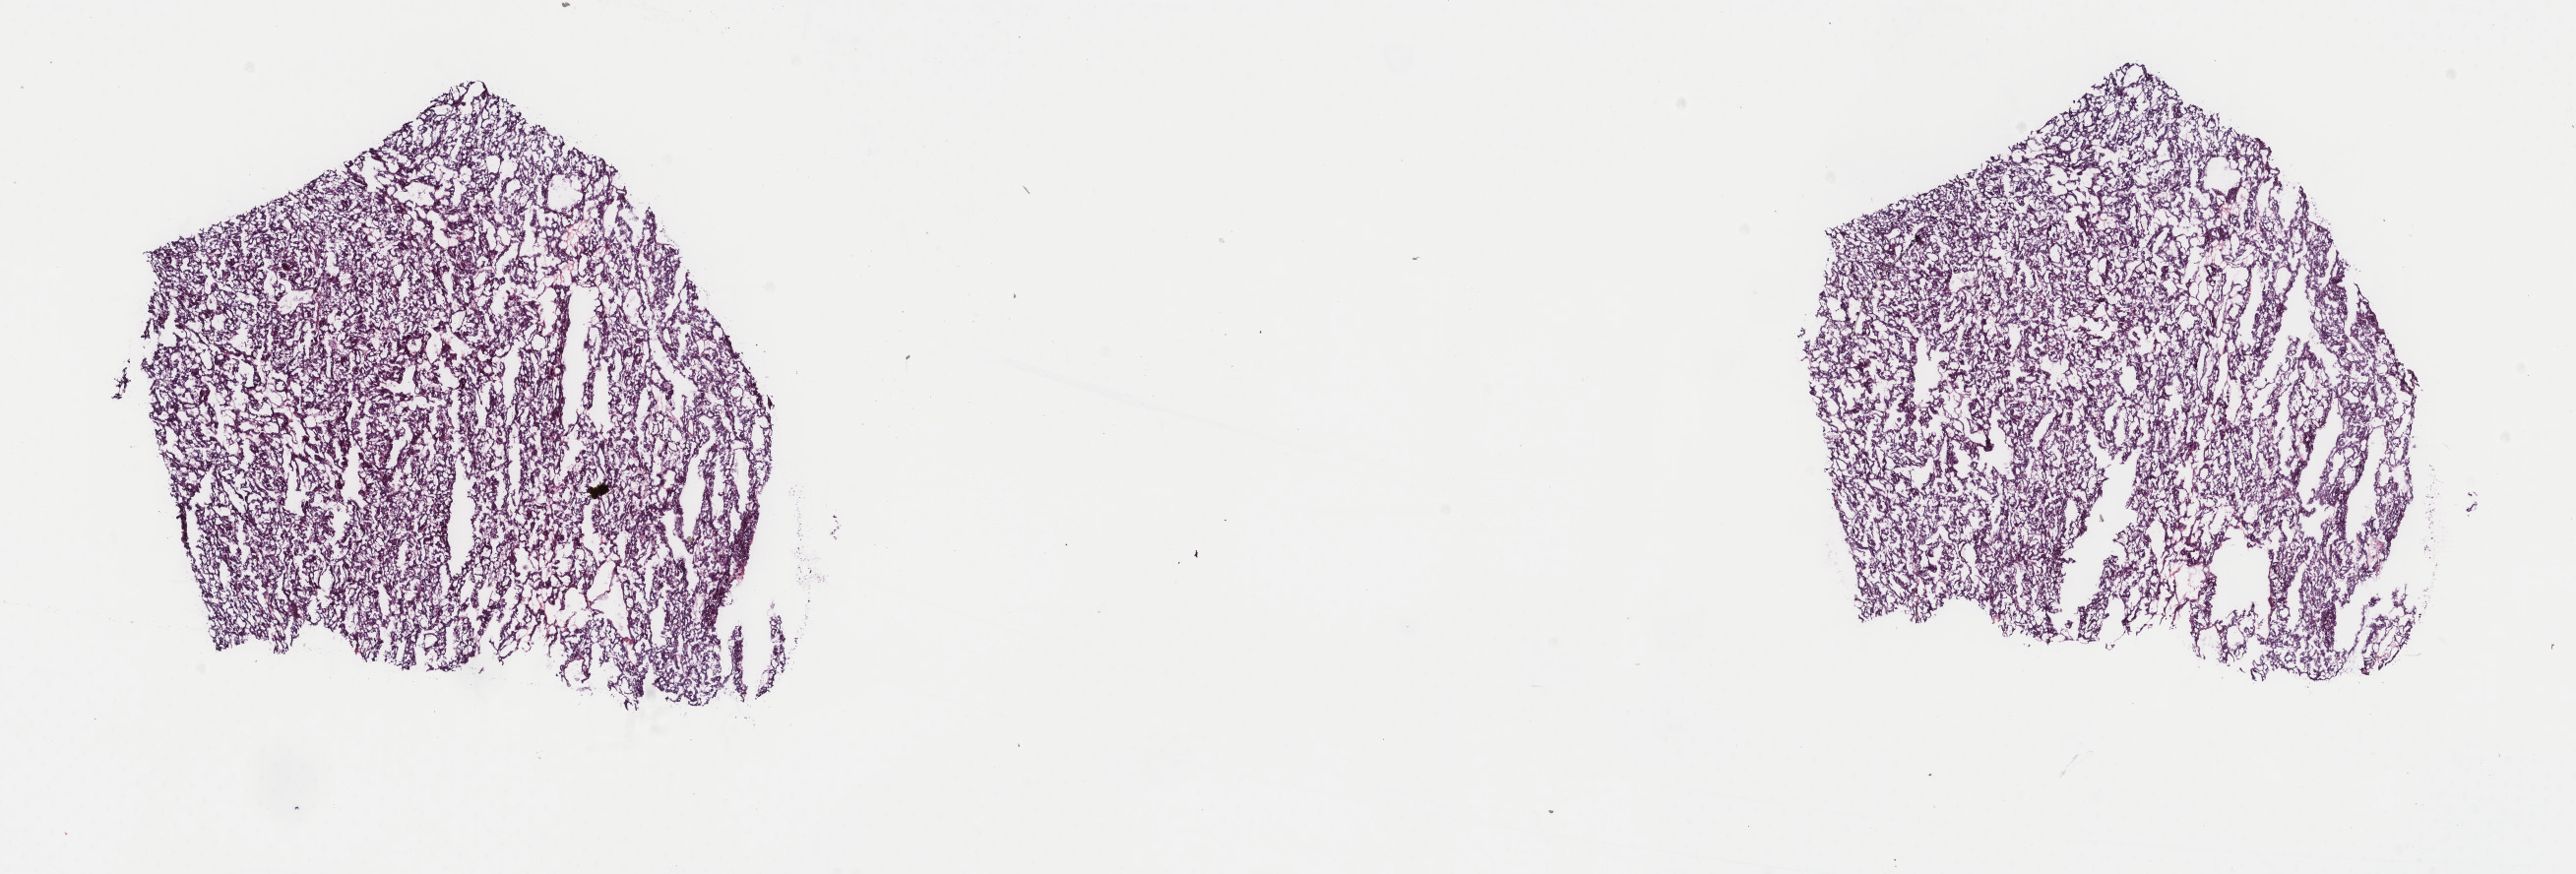
Whole-slide histology image, Hematoxylin and eosin (H&E) stained, shown as a low-resolution overview of the whole scanned area (about 20.8 x 7.0 mm); frozen section from the top of the tissue portion; primary tumour sample from the thyroid. Patient: male, age at initial diagnosis 41 years. Pathologist review of this section (percent, as recorded): tumour cells 90%, tumour nuclei 100%, normal cells 0%, stromal cells 10%, necrosis 0%. Inflammatory infiltration, as recorded: lymphocyte infiltration 0%, monocyte infiltration 1%, neutrophil infiltration 0%.
AJCC pathologic stage: I. Lymph nodes positive (case pathology): 4 of 18 examined. Diagnosis: Papillary adenocarcinoma, NOS (thyroid gland).